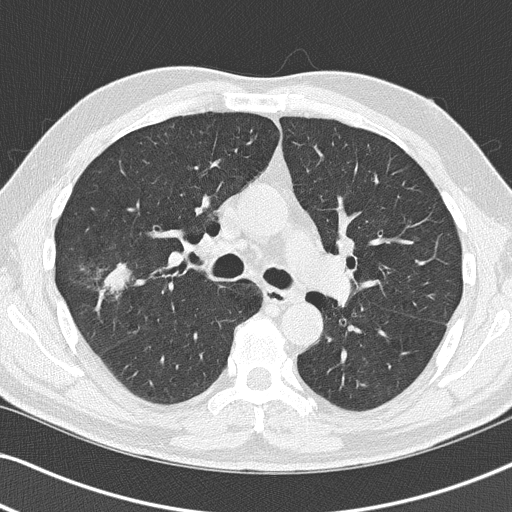
Low-dose screening chest CT, one axial slice. Slice 80 of 140 in the series (ordered by position). Reconstruction kernel B50f. Lung window (W 1500 / L -600 HU). 512 × 512 image matrix, field of view 330 × 330 mm.
Outlined on this slice (manually delineated by an expert):
- lesion 1 (tumor, upper lobe of right lung): box from (x=103, y=263) to (x=131, y=293) px